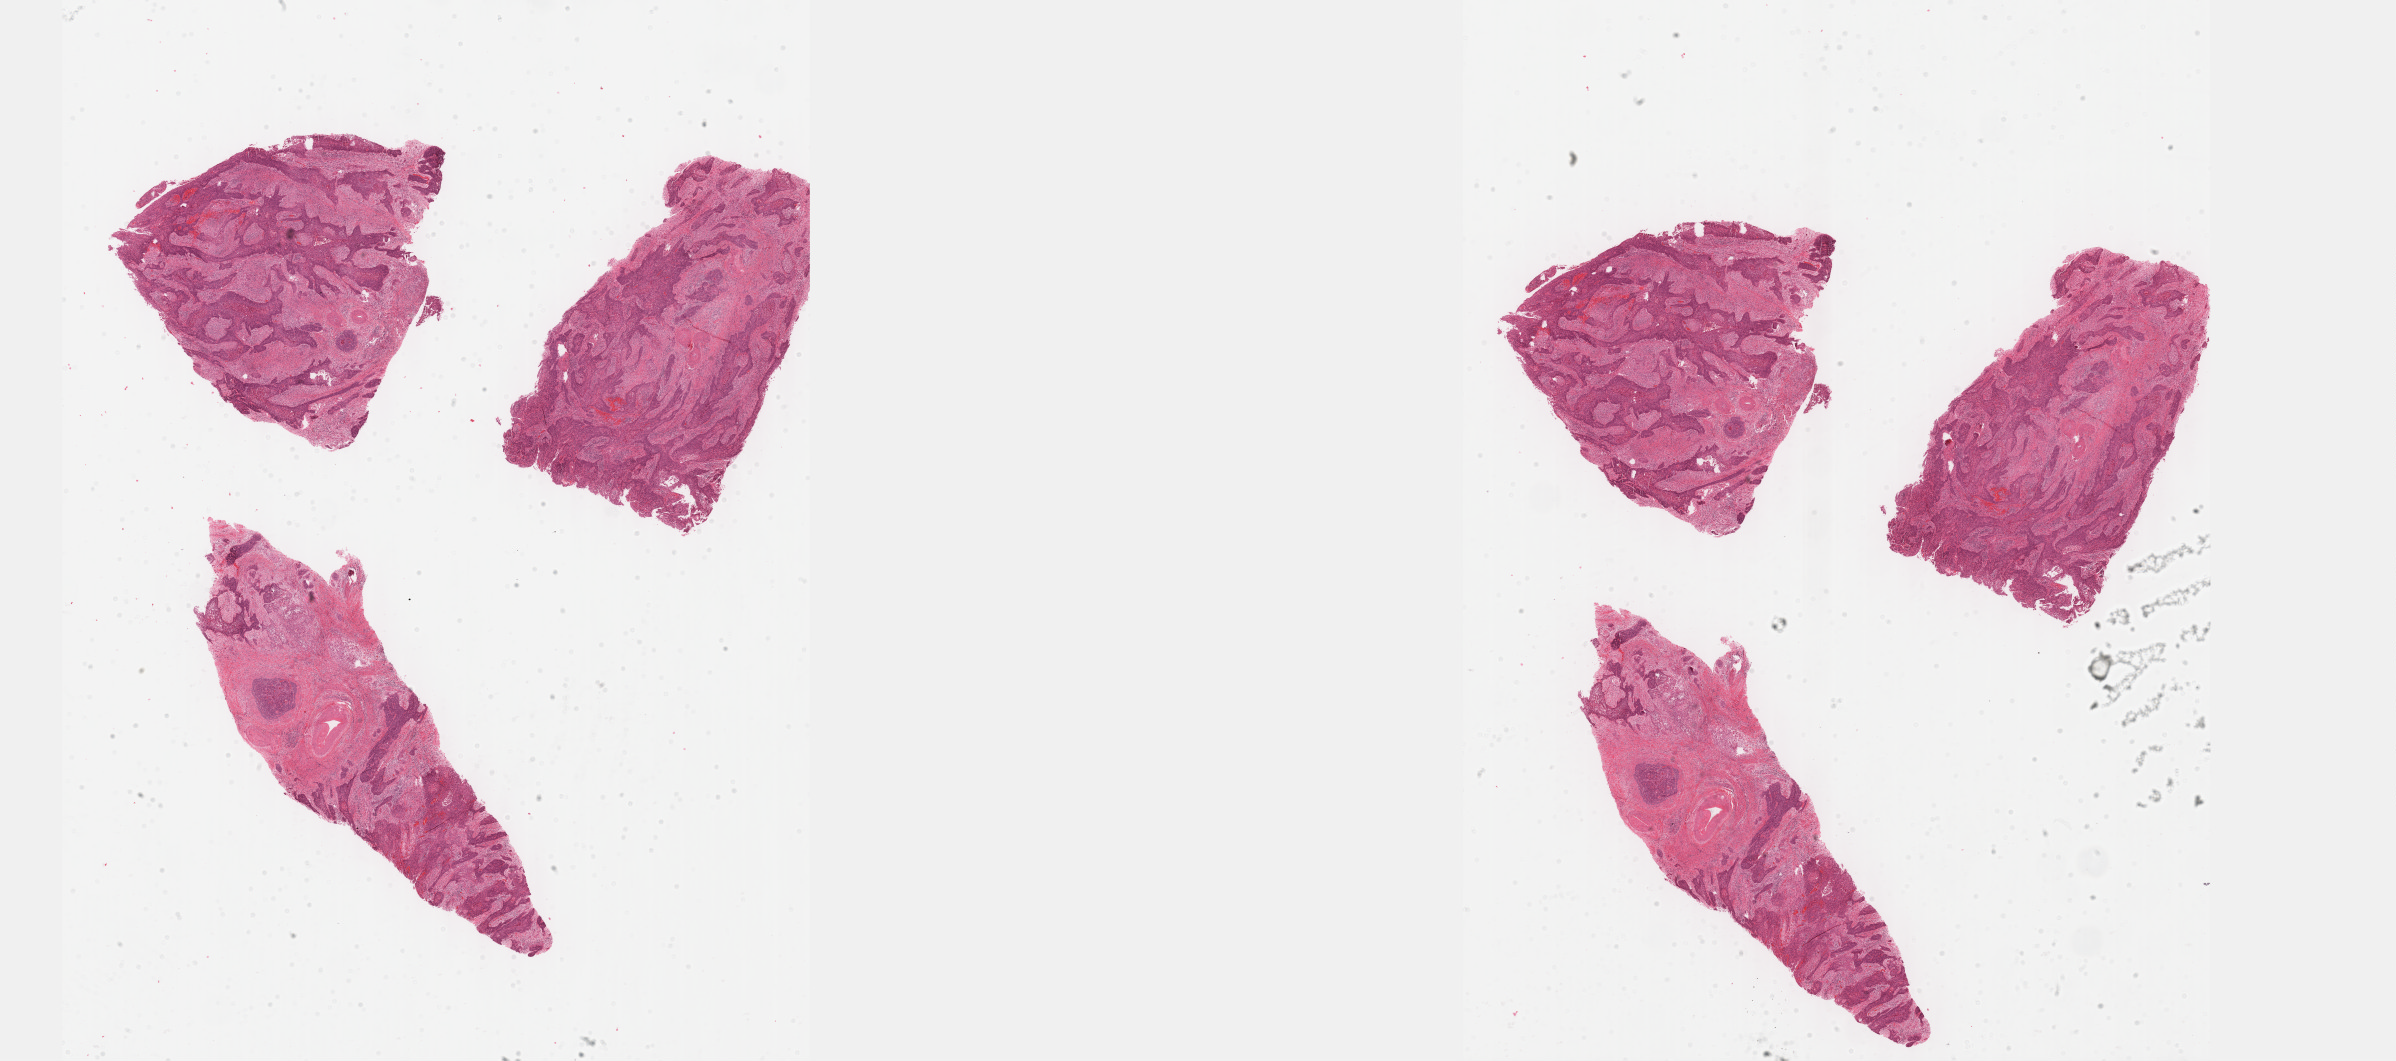
H&E-stained whole-slide image, shown as a low-resolution overview of the whole scanned area (about 38.7 x 17.2 mm, acquisition: 40x scan). Formalin-fixed paraffin-embedded (FFPE) diagnostic section. Primary tumour sample from the cervix. Female patient; age at initial diagnosis 46 years. Histologic grade: G2 (moderately differentiated).
- histologic diagnosis: Squamous cell carcinoma, large cell, nonkeratinizing, NOS (cervix uteri)
- FIGO stage: IB1